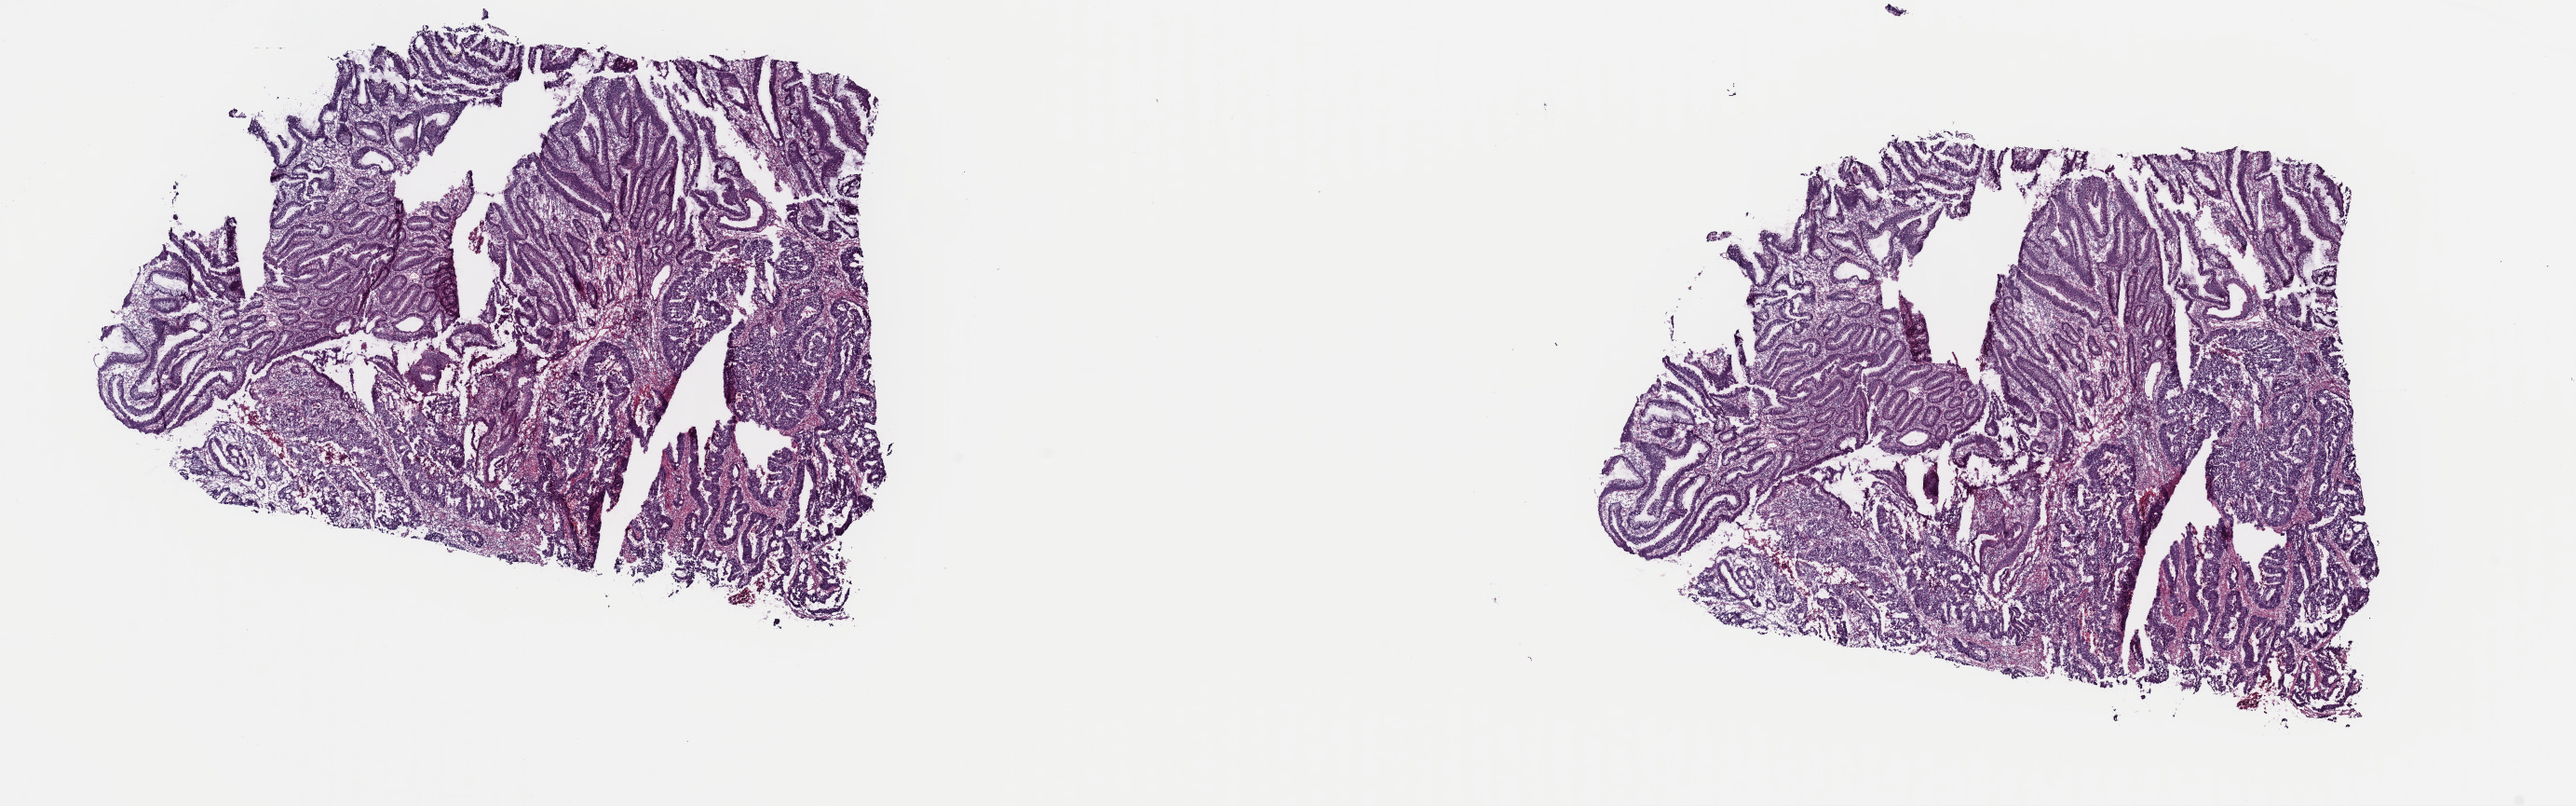
Whole-slide histology image, H&E, low-resolution overview of the scanned area, about 21.9 x 6.8 mm (slide scanned at 40x); frozen section from the top of the tissue portion; colon, primary tumour sample. Female, age 64 years at initial diagnosis. Pathologist review of this section (percent, as recorded): tumour cells 80%, tumour nuclei 75%, normal cells 0%, stromal cells 18%, necrosis 2%. Infiltration values recorded for this section: lymphocyte infiltration 5%, monocyte infiltration 1%, neutrophil infiltration 0%.
Lymph nodes positive (case pathology): 1 of 33 examined. AJCC pathologic stage: IIIC (7th edition). Pathologic diagnosis: Adenocarcinoma, NOS (sigmoid colon).